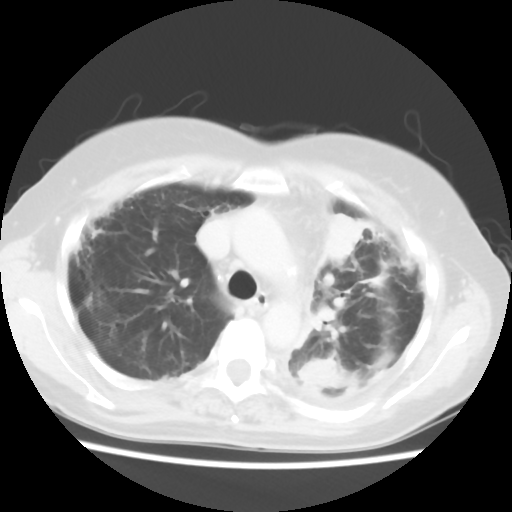
Chest CT, one axial slice; position 40 of 56 along the scan axis; reconstruction kernel STANDARD; 120 kVp; lung window (W 1500 / L -600 HU); 512 × 512 image matrix. Female patient, age 56 years. Case-level facts recorded for this patient, not image findings: clinical TNM (as recorded): T1c N0 M1.
Outlined on this slice (rectangle marked by the reading radiologist):
- lung tumour (recorded histology: adenocarcinoma): box from (x=316, y=203) to (x=369, y=274) px